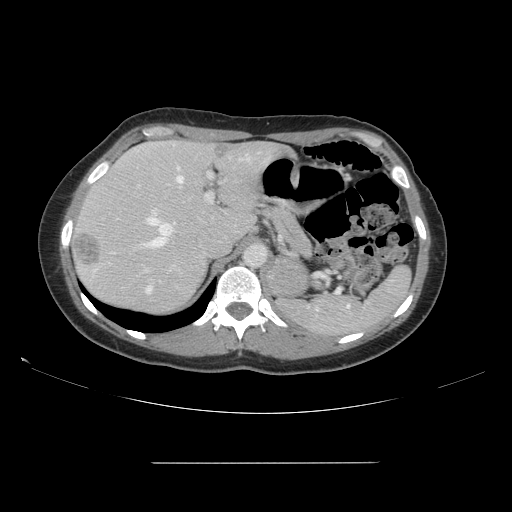
Contrast-enhanced abdominal CT, one axial slice. Position 110 of 151 along the scan axis. 120 kVp. Intravenous contrast given. Soft-tissue window (W 400 / L 40 HU). 512 × 512 image matrix. Female patient, age 46 years. From the clinical record (not read from this slice): diagnosis: colorectal cancer liver metastases, imaged before liver resection; multiple liver metastases: yes; largest metastasis: 3 cm.
Outlined on this slice (expert manual segmentation):
- hepatic veins: box from (x=94, y=153) to (x=251, y=272) px
- liver: (x=70, y=141)–(x=286, y=315)
- planned liver remnant (the part of the liver to remain after resection): (x=88, y=141)–(x=287, y=252)
- portal vein (with intrahepatic branches): (x=138, y=174)–(x=213, y=294)
- liver metastasis: (x=74, y=234)–(x=103, y=268)
- liver metastasis: (x=214, y=146)–(x=229, y=159)